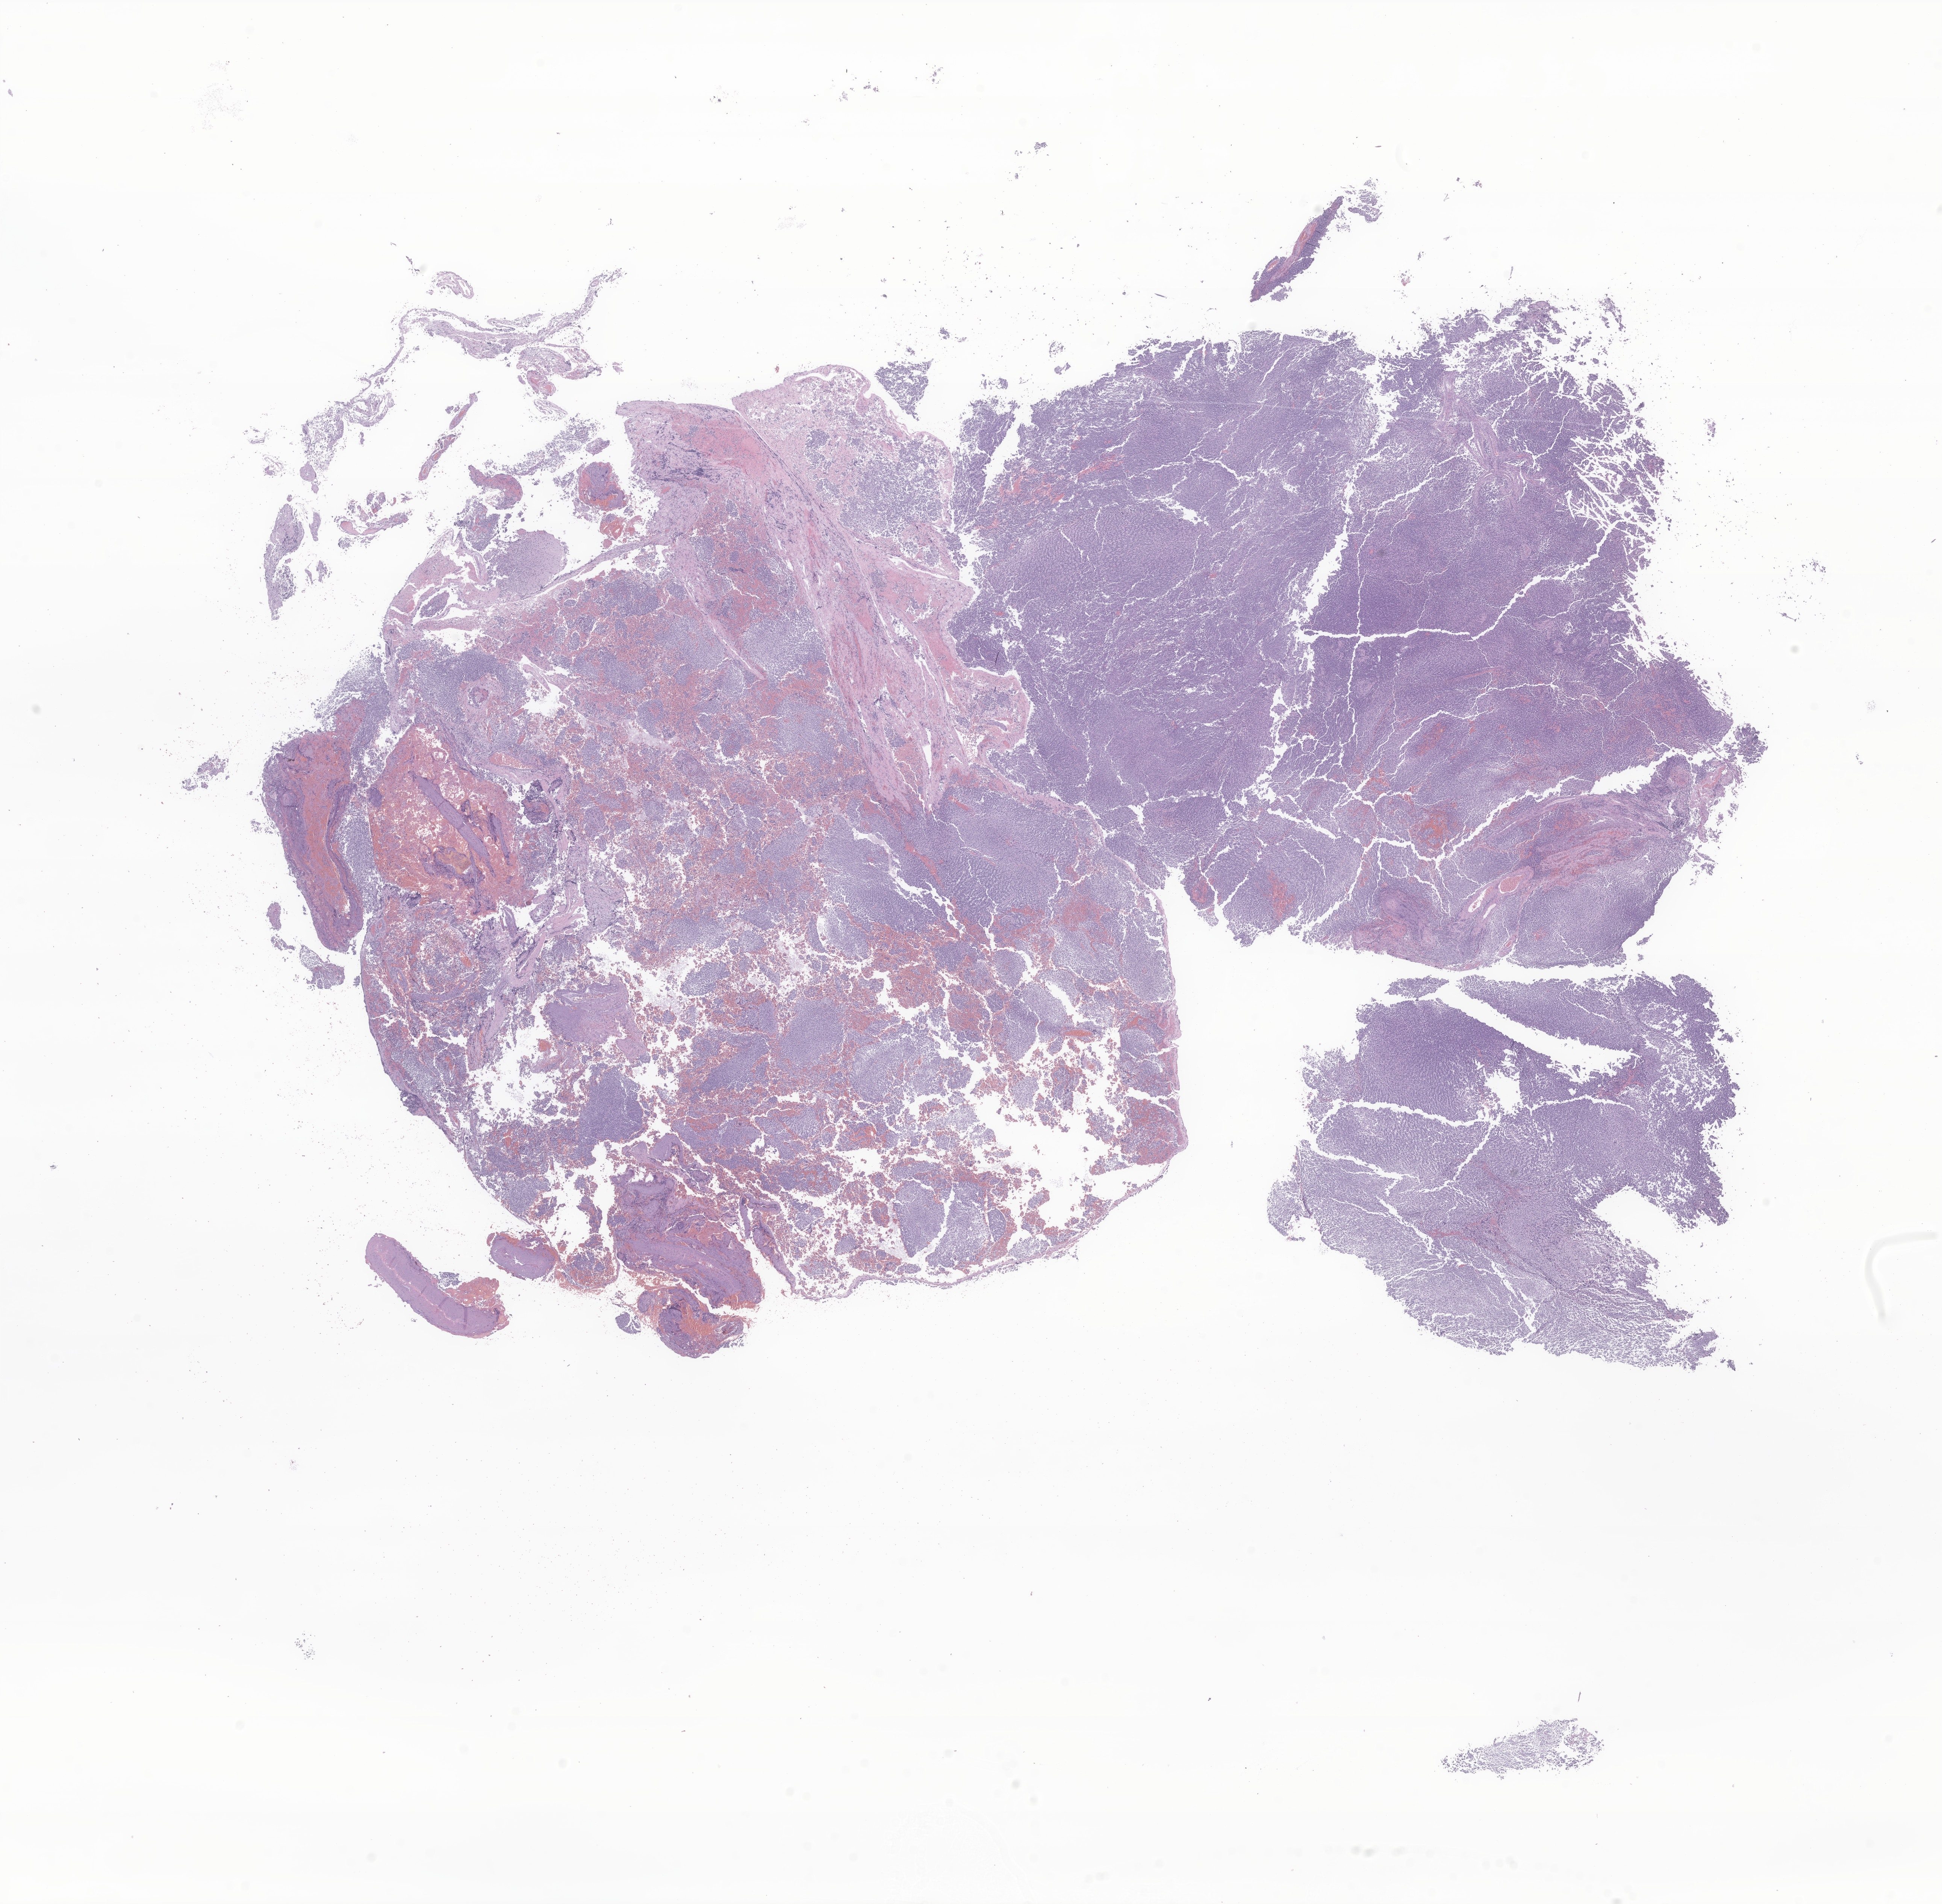
Digitized haematoxylin and eosin-stained section of tumor tissue from the cerebellum, low-resolution overview of the scanned area, about 21.8 x 21.4 mm, formalin-fixed paraffin-embedded section. Patient male; age 164 months (13 years 8 months).
- recorded diagnosis: Medulloblastoma, NOS